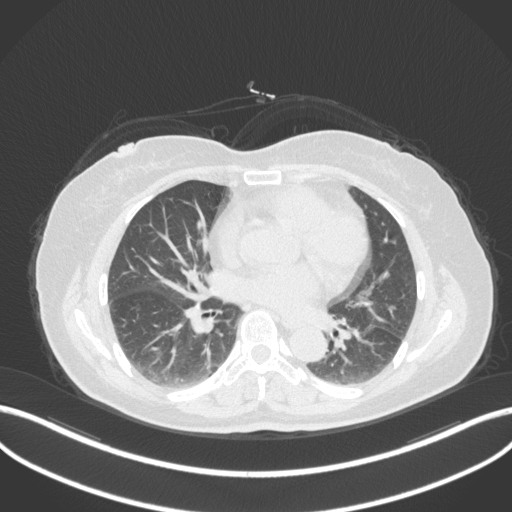
Chest CT, one axial slice; position 176 of 307 along the scan axis; lung window (W 1500 / L -600 HU); 1 mm slice thickness; 512 × 512 image matrix. Patient: female, 59 years. From the clinical record (not read from this slice): clinical TNM (as recorded): T2a N0 M0.
Outlined on this slice (bounding box drawn by a radiologist):
- lung tumour (recorded histology: adenocarcinoma): bounding box (x1, y1, x2, y2) in pixels: (353, 325, 379, 355)